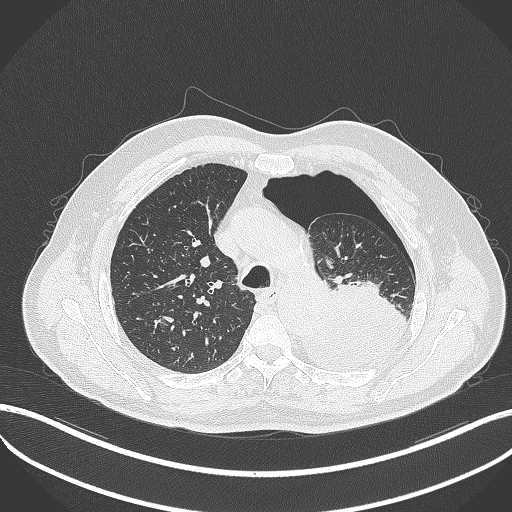
Chest CT, one axial slice; position 371 of 464 along the scan axis; lung window (W 1500 / L -600 HU); 512 × 512 image matrix, field of view 400 × 400 mm. Patient: male, 76 years. From the clinical record (not read from this slice): clinical TNM (as recorded): T3 N0 M1b.
Structures marked on this image (rectangle marked by the reading radiologist):
- lung tumour (recorded histology: adenocarcinoma): box from (x=298, y=280) to (x=412, y=372) px